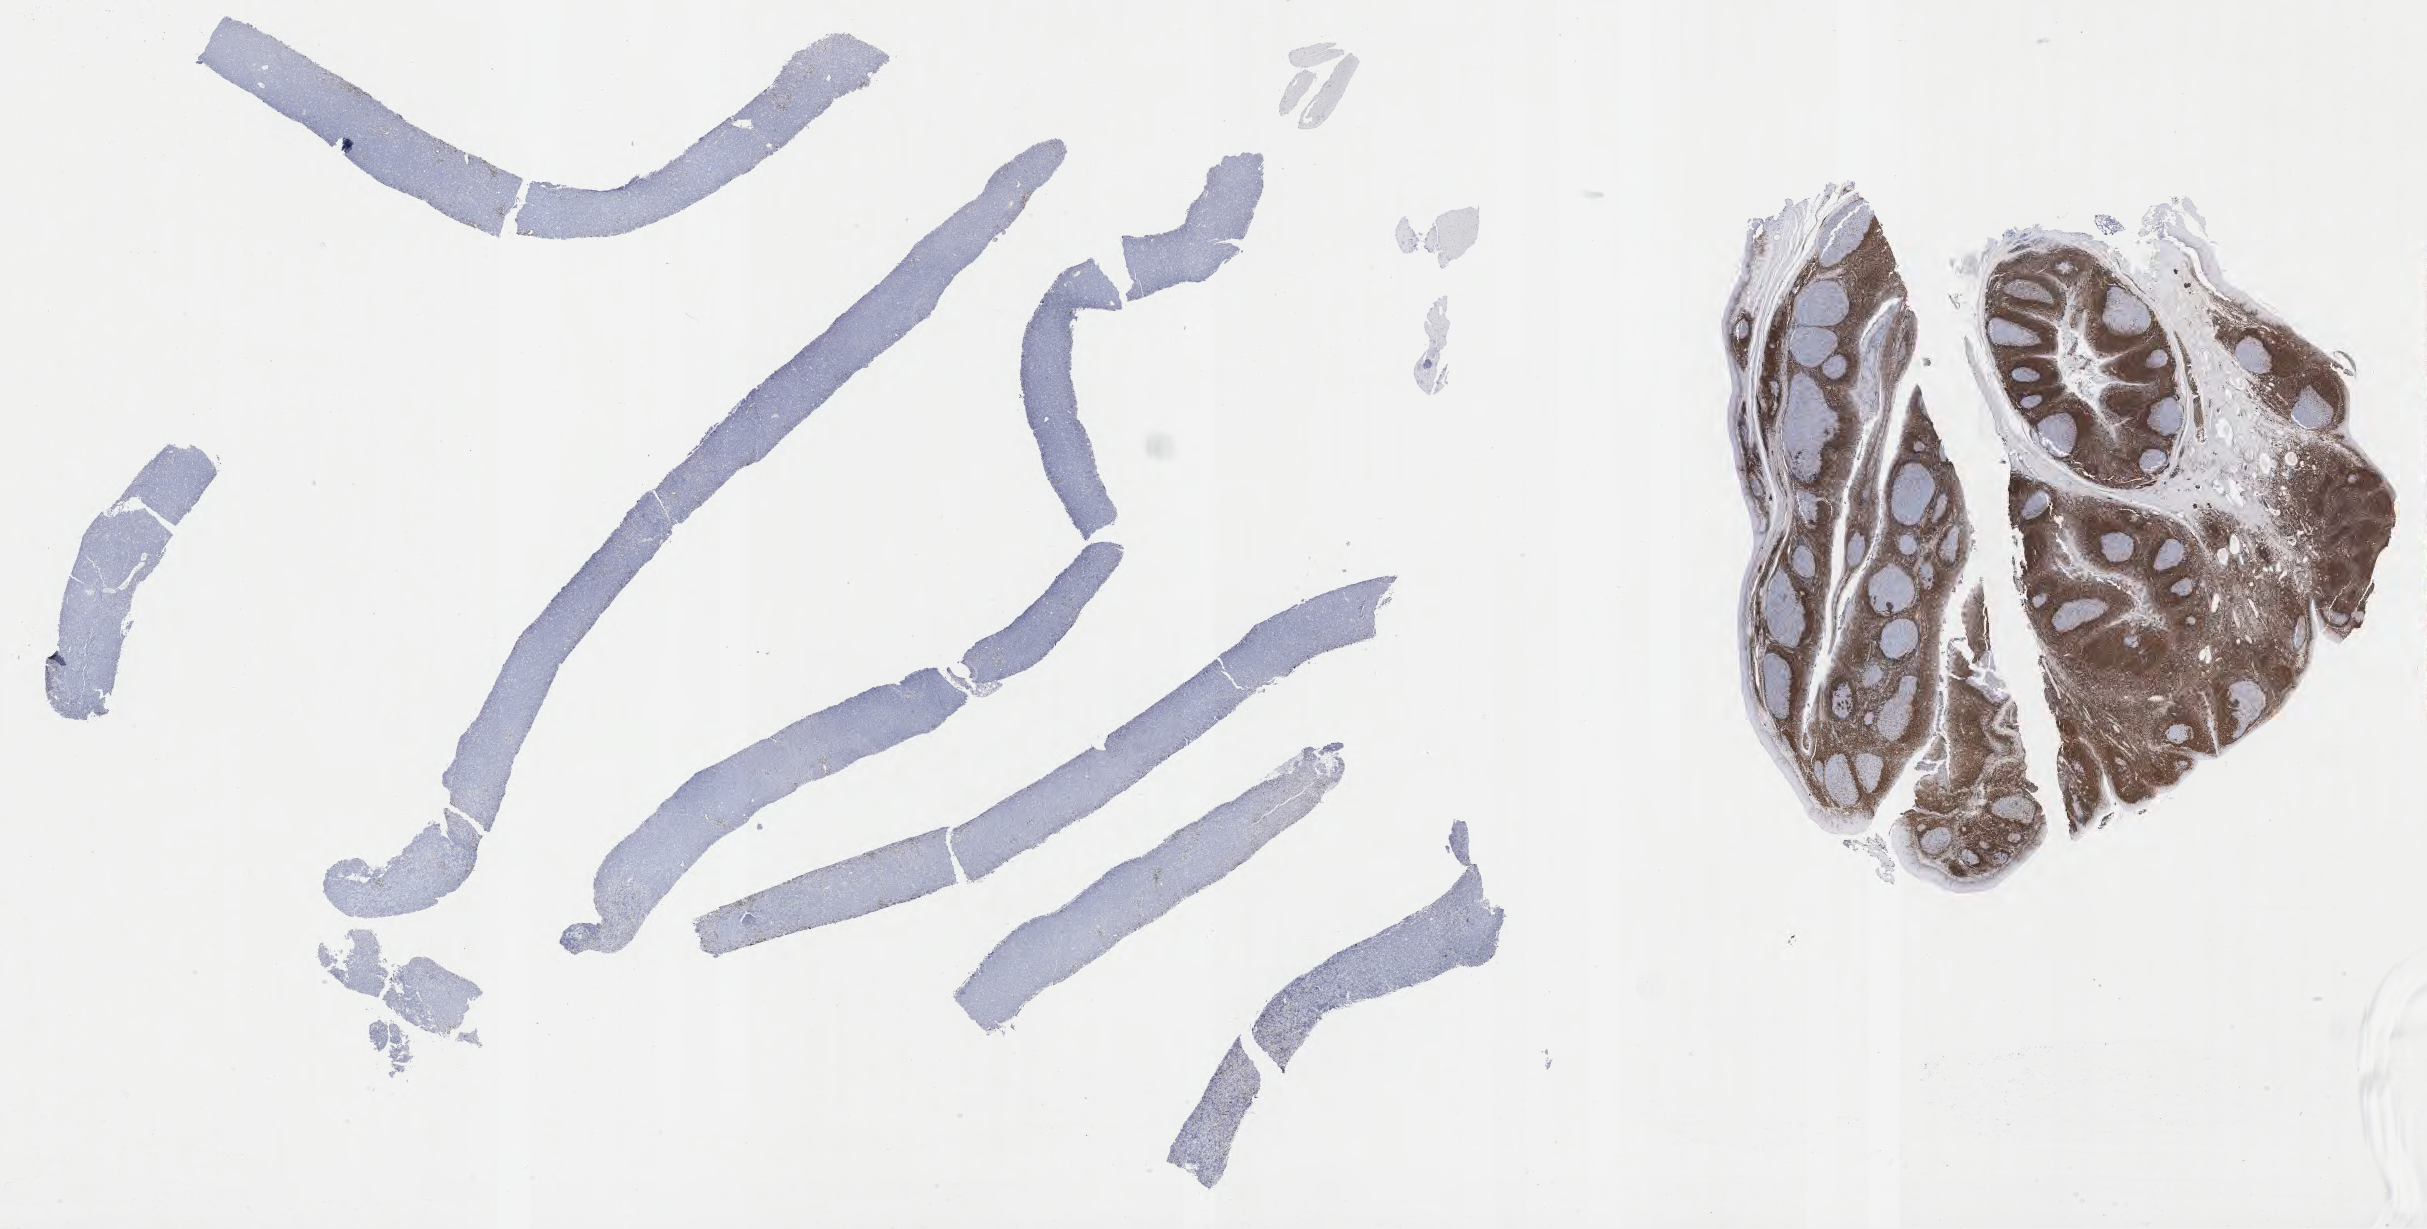
Immunohistochemistry (IHC) whole-slide image stained for BCL2 — shown as a low-resolution overview of the whole scanned area (about 39.3 x 19.9 mm); tumor tissue. Patient: male, 29 years old.
Diagnosis: Burkitt lymphoma, NOS.